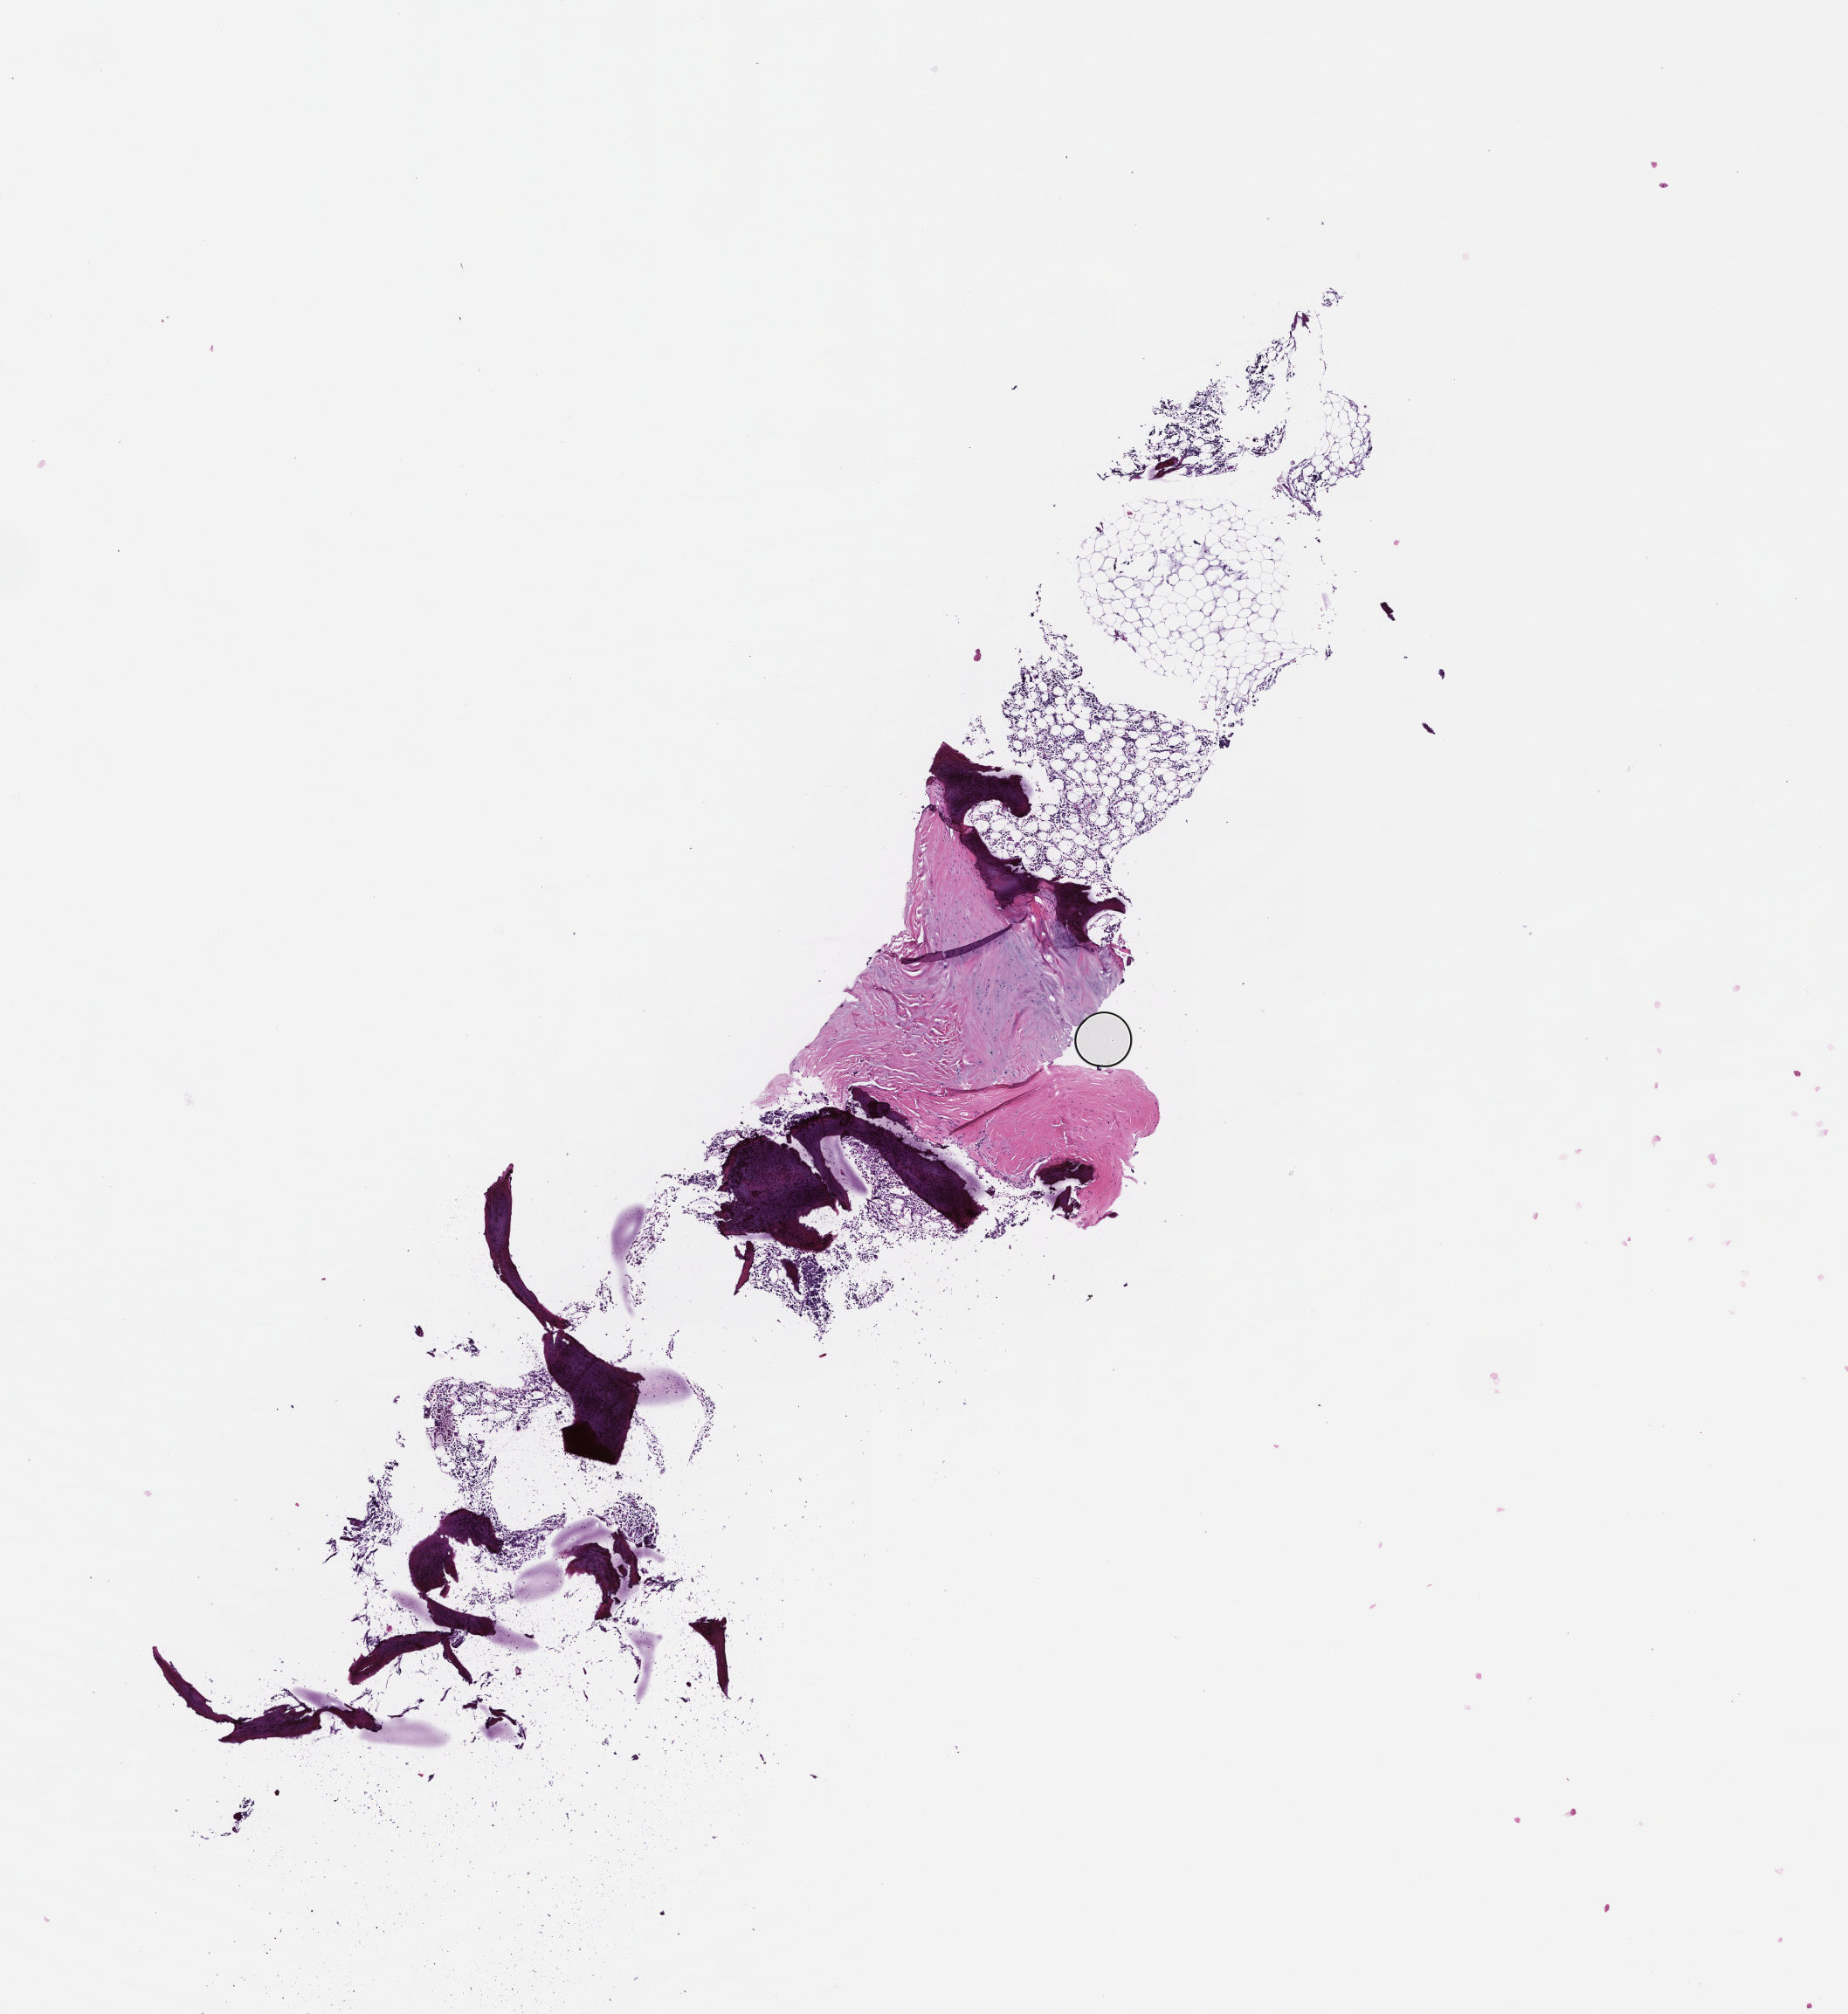
Whole-slide image, H&E stain, a low-resolution overview of the entire scanned area, about 8.5 x 9.3 mm; formalin-fixed, paraffin-embedded (FFPE) tissue; site: bone marrow. Patient sex: female.
This section: primary tumour tissue. Diagnosis: Plasma Cell Myeloma.